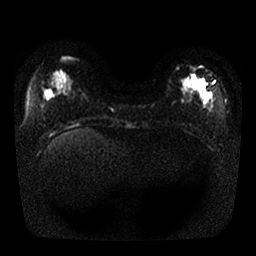
Breast MRI, one axial slice. Position 9 of 25 along the scan axis. Diffusion-weighted series; image 2 of 4 stored at this slice position (different b-values; order by instance number). 1.5 T. 256 × 256 image matrix. Female patient.
Outlined on this slice (outlined manually by an expert reader):
- tumour on diffusion-weighted imaging: bounding box [x1, y1, x2, y2] px = [184, 77, 205, 87]